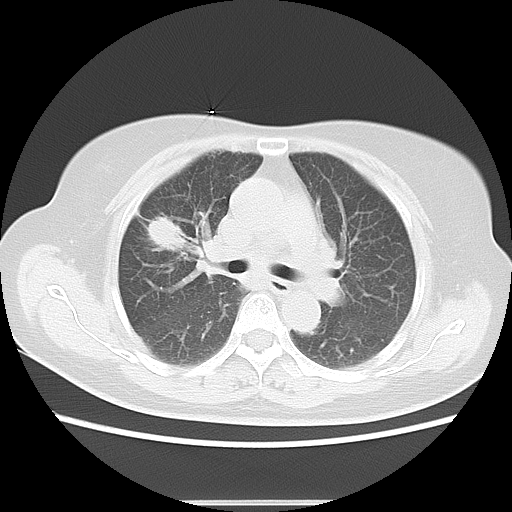
Chest CT, one axial slice. Position 8 of 17 along the scan axis. Reconstruction kernel LUNG. Lung window (W 1500 / L -600 HU). 5 mm slice thickness. 512 × 512 image matrix, field of view 350 × 350 mm. Female patient, age 57 years. From the clinical record (not read from this slice): clinical TNM (as recorded): T1c N1 M0.
Outlined on this slice (rectangle marked by the reading radiologist):
- lung tumour (recorded histology: adenocarcinoma): box from (x=143, y=210) to (x=188, y=260) px